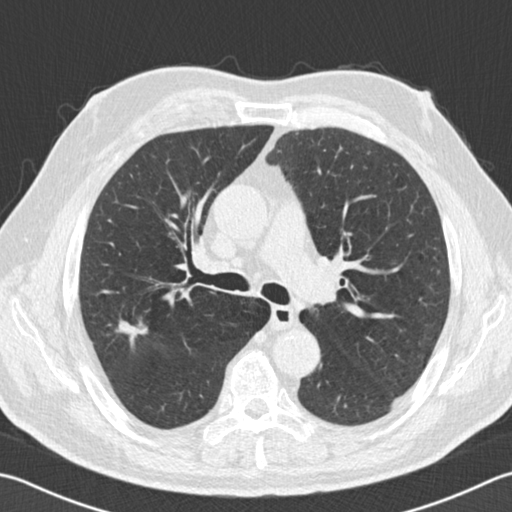
Low-dose screening chest CT, one axial slice; 120 kVp; lung window (W 1500 / L -600 HU); 2 mm slice thickness; 512 × 512 image matrix, field of view 346 × 346 mm.
Outlined on this slice (manually delineated by an expert):
- lesion 1 (tumor, upper lobe of right lung): box from (x=119, y=321) to (x=147, y=345) px